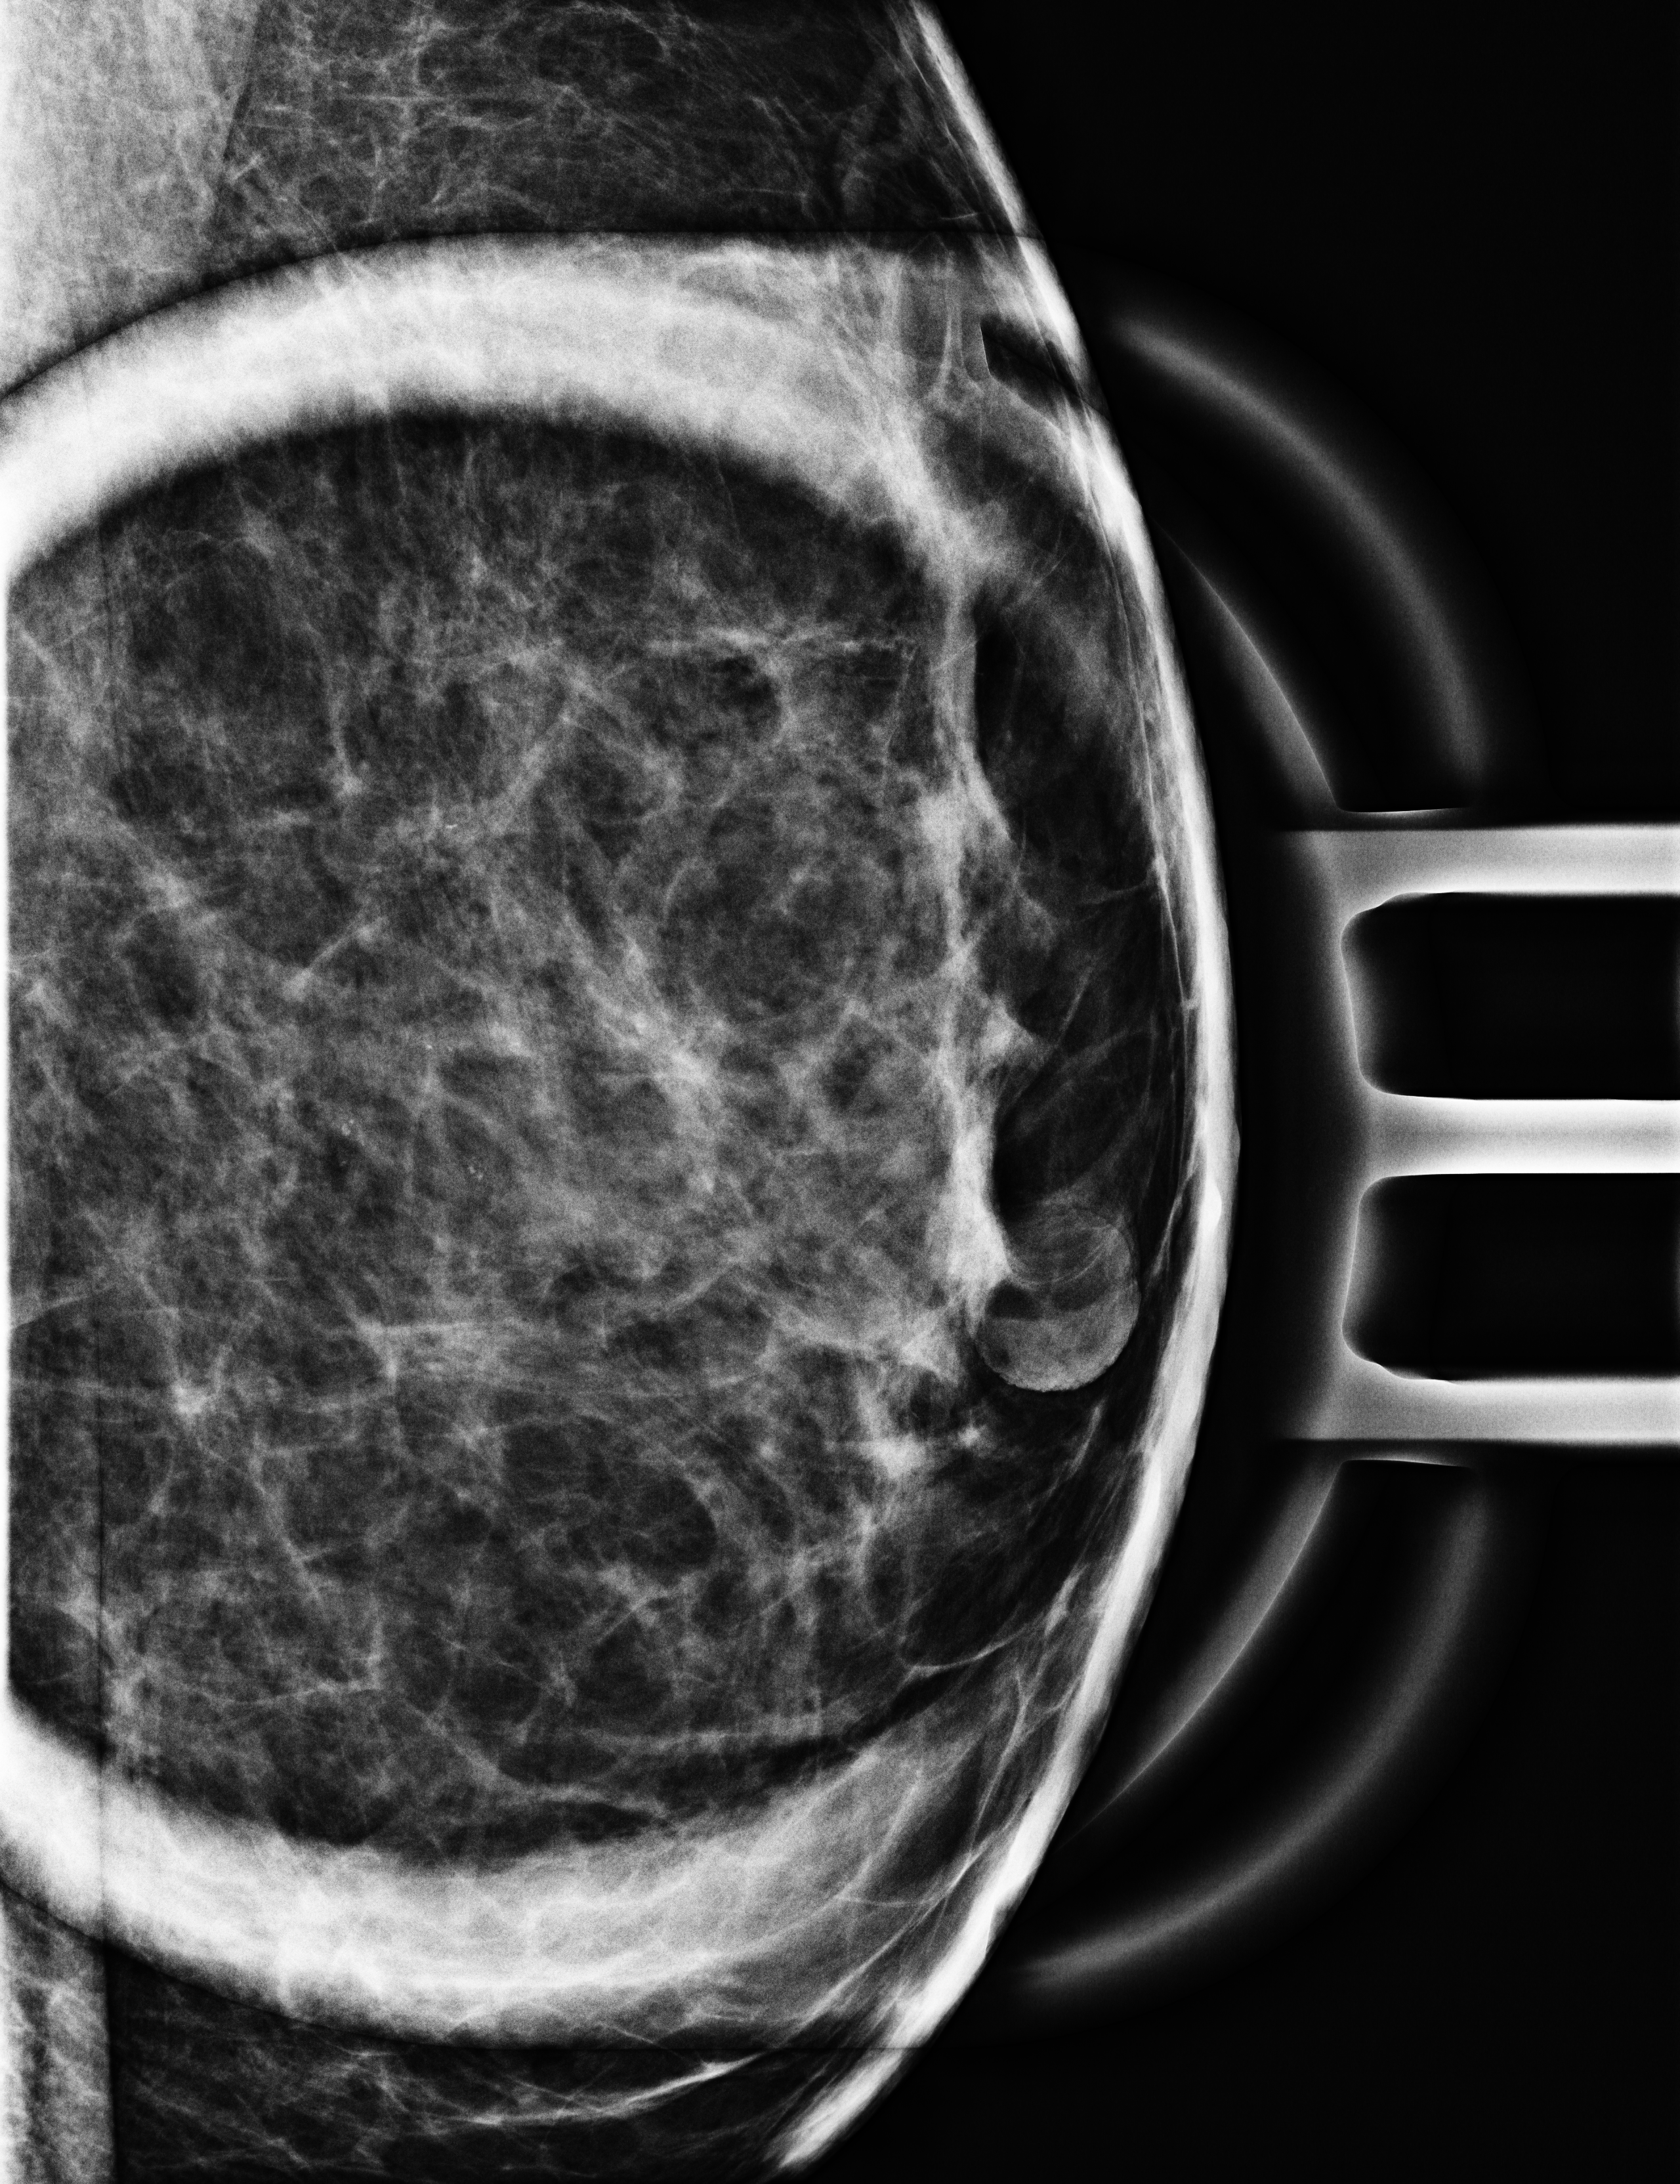
Additional work-up view; compressed breast thickness 43 mm. Patient: female, 46 years.
Image type: full-field digital mammogram. Breast: left. Projection: mediolateral (ML) view, magnification.